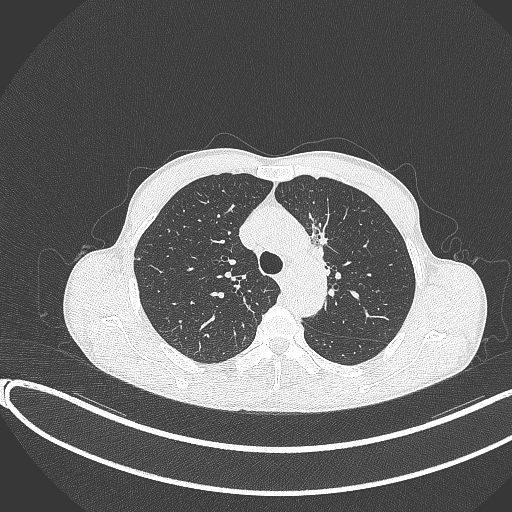
Chest CT, one axial slice; position 273 of 374 along the scan axis; reconstruction kernel B70f; 120 kVp; lung window (W 1500 / L -600 HU); 1 mm slice thickness; 512 × 512 image matrix, field of view 400 × 400 mm. Patient: male, 58 years. Case-level facts recorded for this patient, not image findings: clinical TNM (as recorded): T1c N1 M0.
Outlined on this slice (bounding box drawn by a radiologist):
- lung tumour (recorded histology: adenocarcinoma): bounding box (x1, y1, x2, y2) in pixels: (301, 215, 340, 273)